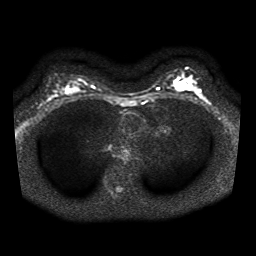
Breast MRI, one axial slice; position 23 of 41 along the scan axis; diffusion-weighted series; image 2 of 4 stored at this slice position (different b-values; order by instance number); 1.5 T; 5 mm slice thickness; 256 × 256 image matrix, field of view 320 × 320 mm. Female patient.
Annotated regions visible in this slice (manually delineated by an expert):
- tumour on diffusion-weighted imaging: bounding box <188,81,193,88> (left, top, right, bottom; pixels)